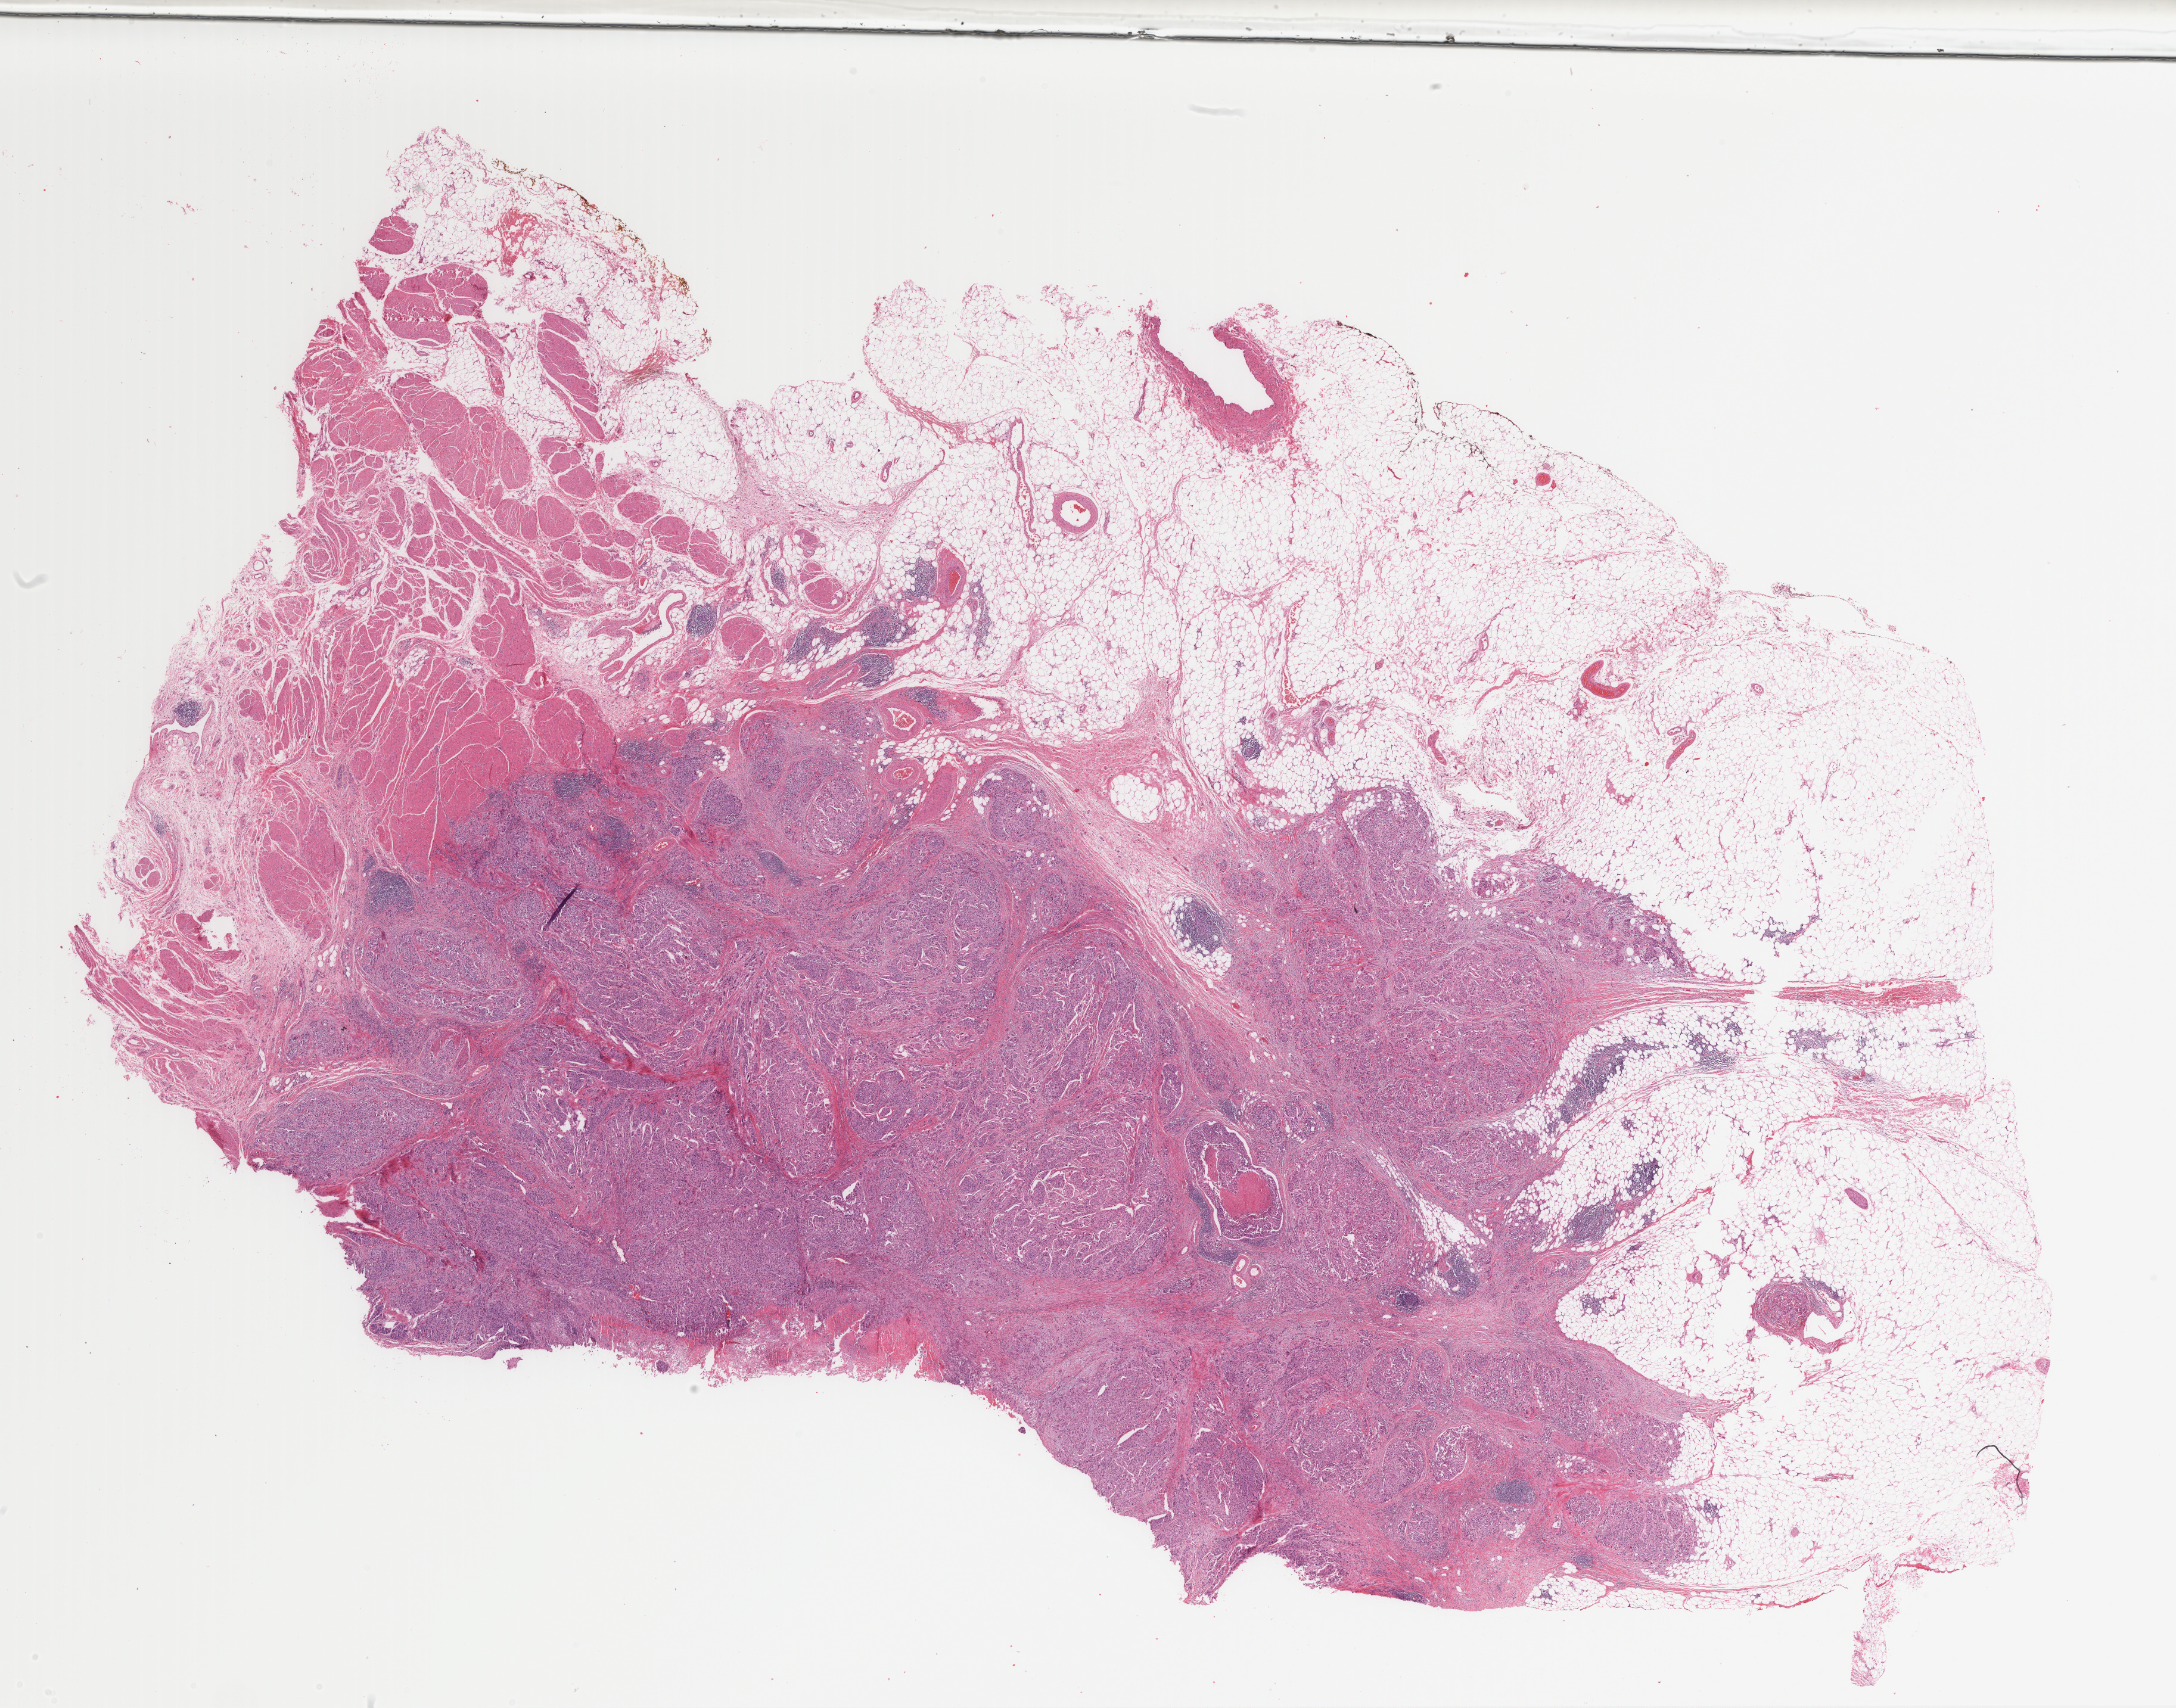
Digitized H&E tissue section (whole slide) — low-resolution overview of the scanned area, about 29.0 x 22.7 mm (from a 40x scan); FFPE section; primary tumour sample from the bladder. Male, age 79 years at initial diagnosis. Histologic grade: high grade.
Lymph nodes positive (case pathology): 12 of 37 examined. AJCC pathologic stage: IV (7th edition). Histologic diagnosis: Transitional cell carcinoma.